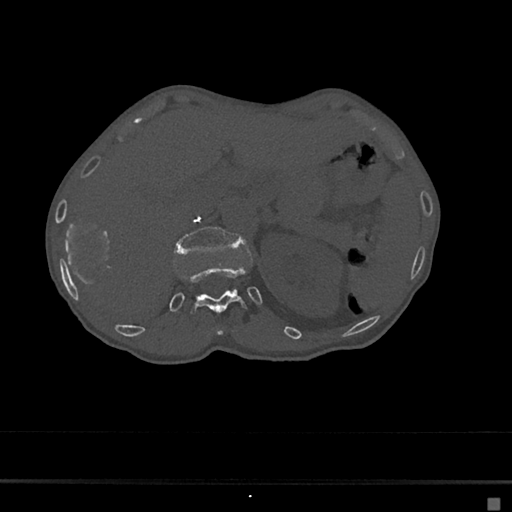
CT including the spine, one axial slice; position 116 of 797 along the scan axis; bone window (W 1800 / L 400 HU); 0.5 mm slice thickness; 512 × 512 image matrix, field of view 360 × 360 mm. Patient: female, 68 years. Case-level facts recorded for this patient, not image findings: primary cancer: renal.
Annotated regions visible in this slice (semi-automatic segmentation, software-assisted and operator-edited):
- L1 vertebra: box from (x=173, y=226) to (x=244, y=255) px
- T11 vertebra: (x=216, y=330)–(x=223, y=336)
- T12 vertebra: (x=184, y=265)–(x=248, y=316)